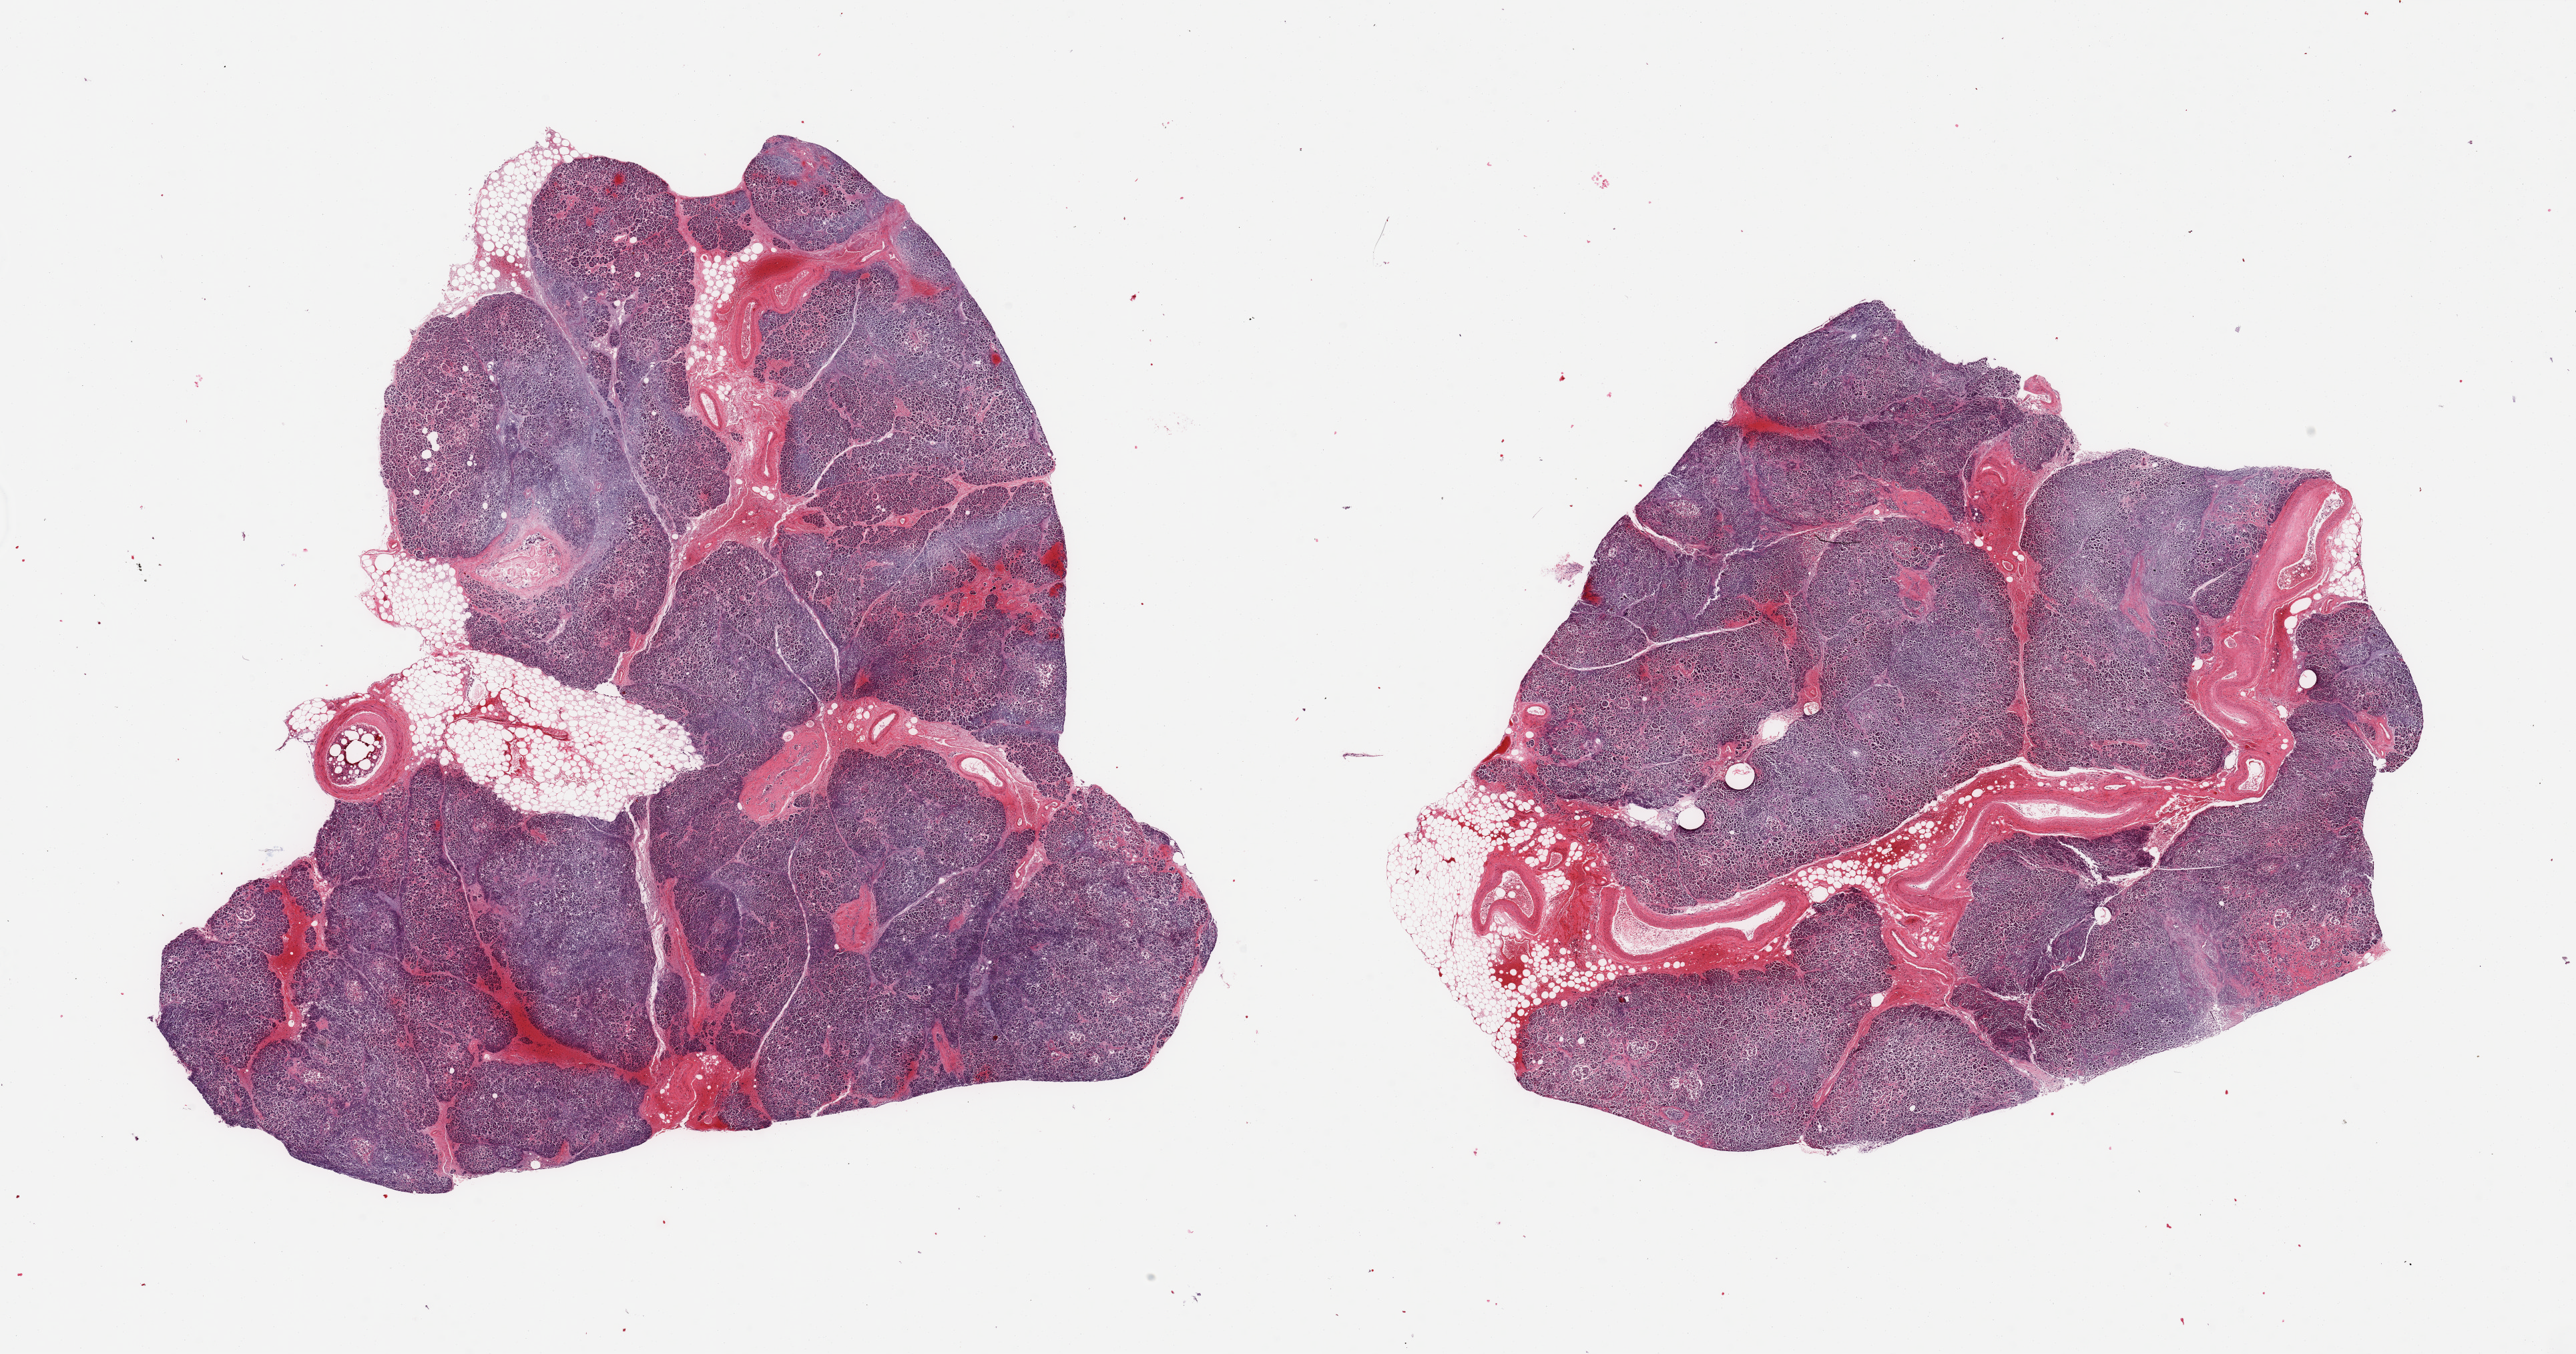
H&E whole-slide image — shown as a low-resolution overview of the whole scanned area (about 30.5 x 16.0 mm, acquisition: 20x scan), PAXgene-fixed, paraffin-embedded tissue, sampled site (target tissue): pancreas, donor tissue sample. Donor: female.
Review note (as recorded): 2 pieces: large vessels in one, 10% internall fat in the other.